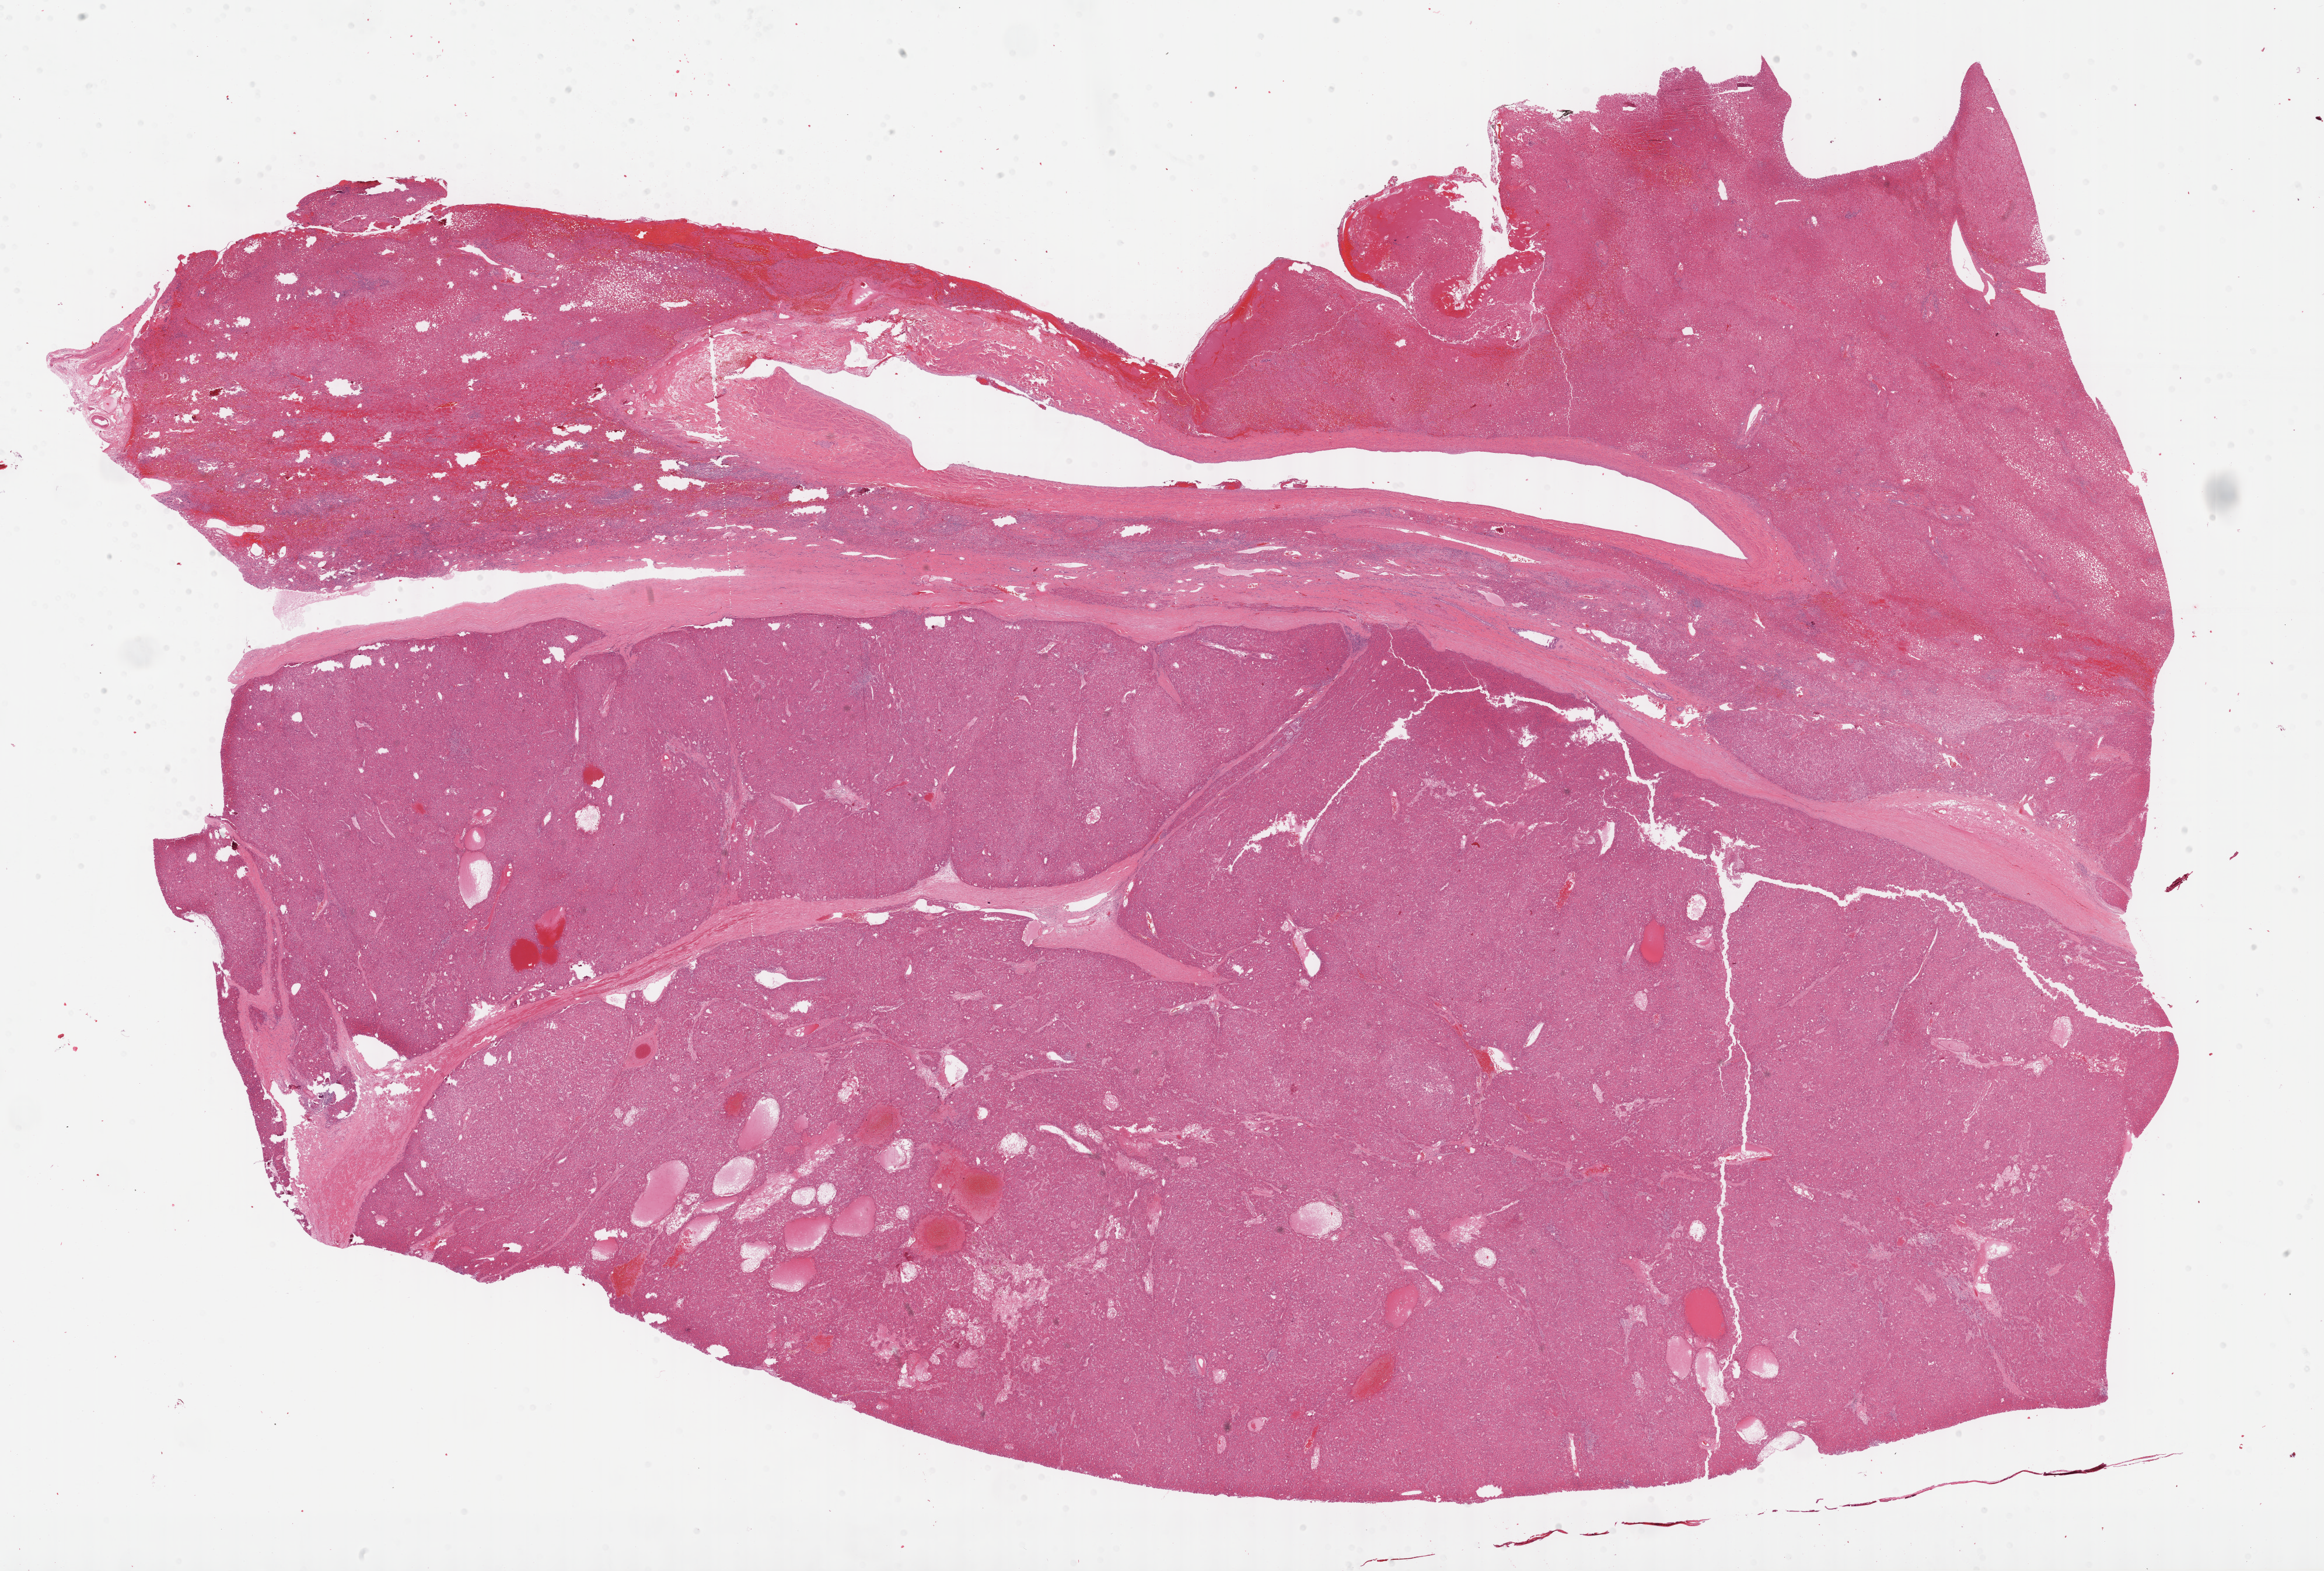
H&E whole-slide image, whole scanned area (about 32.2 x 21.8 mm, from a 40x scan) shown as a low-resolution overview, FFPE section, sample: primary tumour, liver. Female, age 64 years at initial diagnosis. Histologic grade: G1 (well differentiated).
Pathologic diagnosis: Hepatocellular carcinoma, NOS.